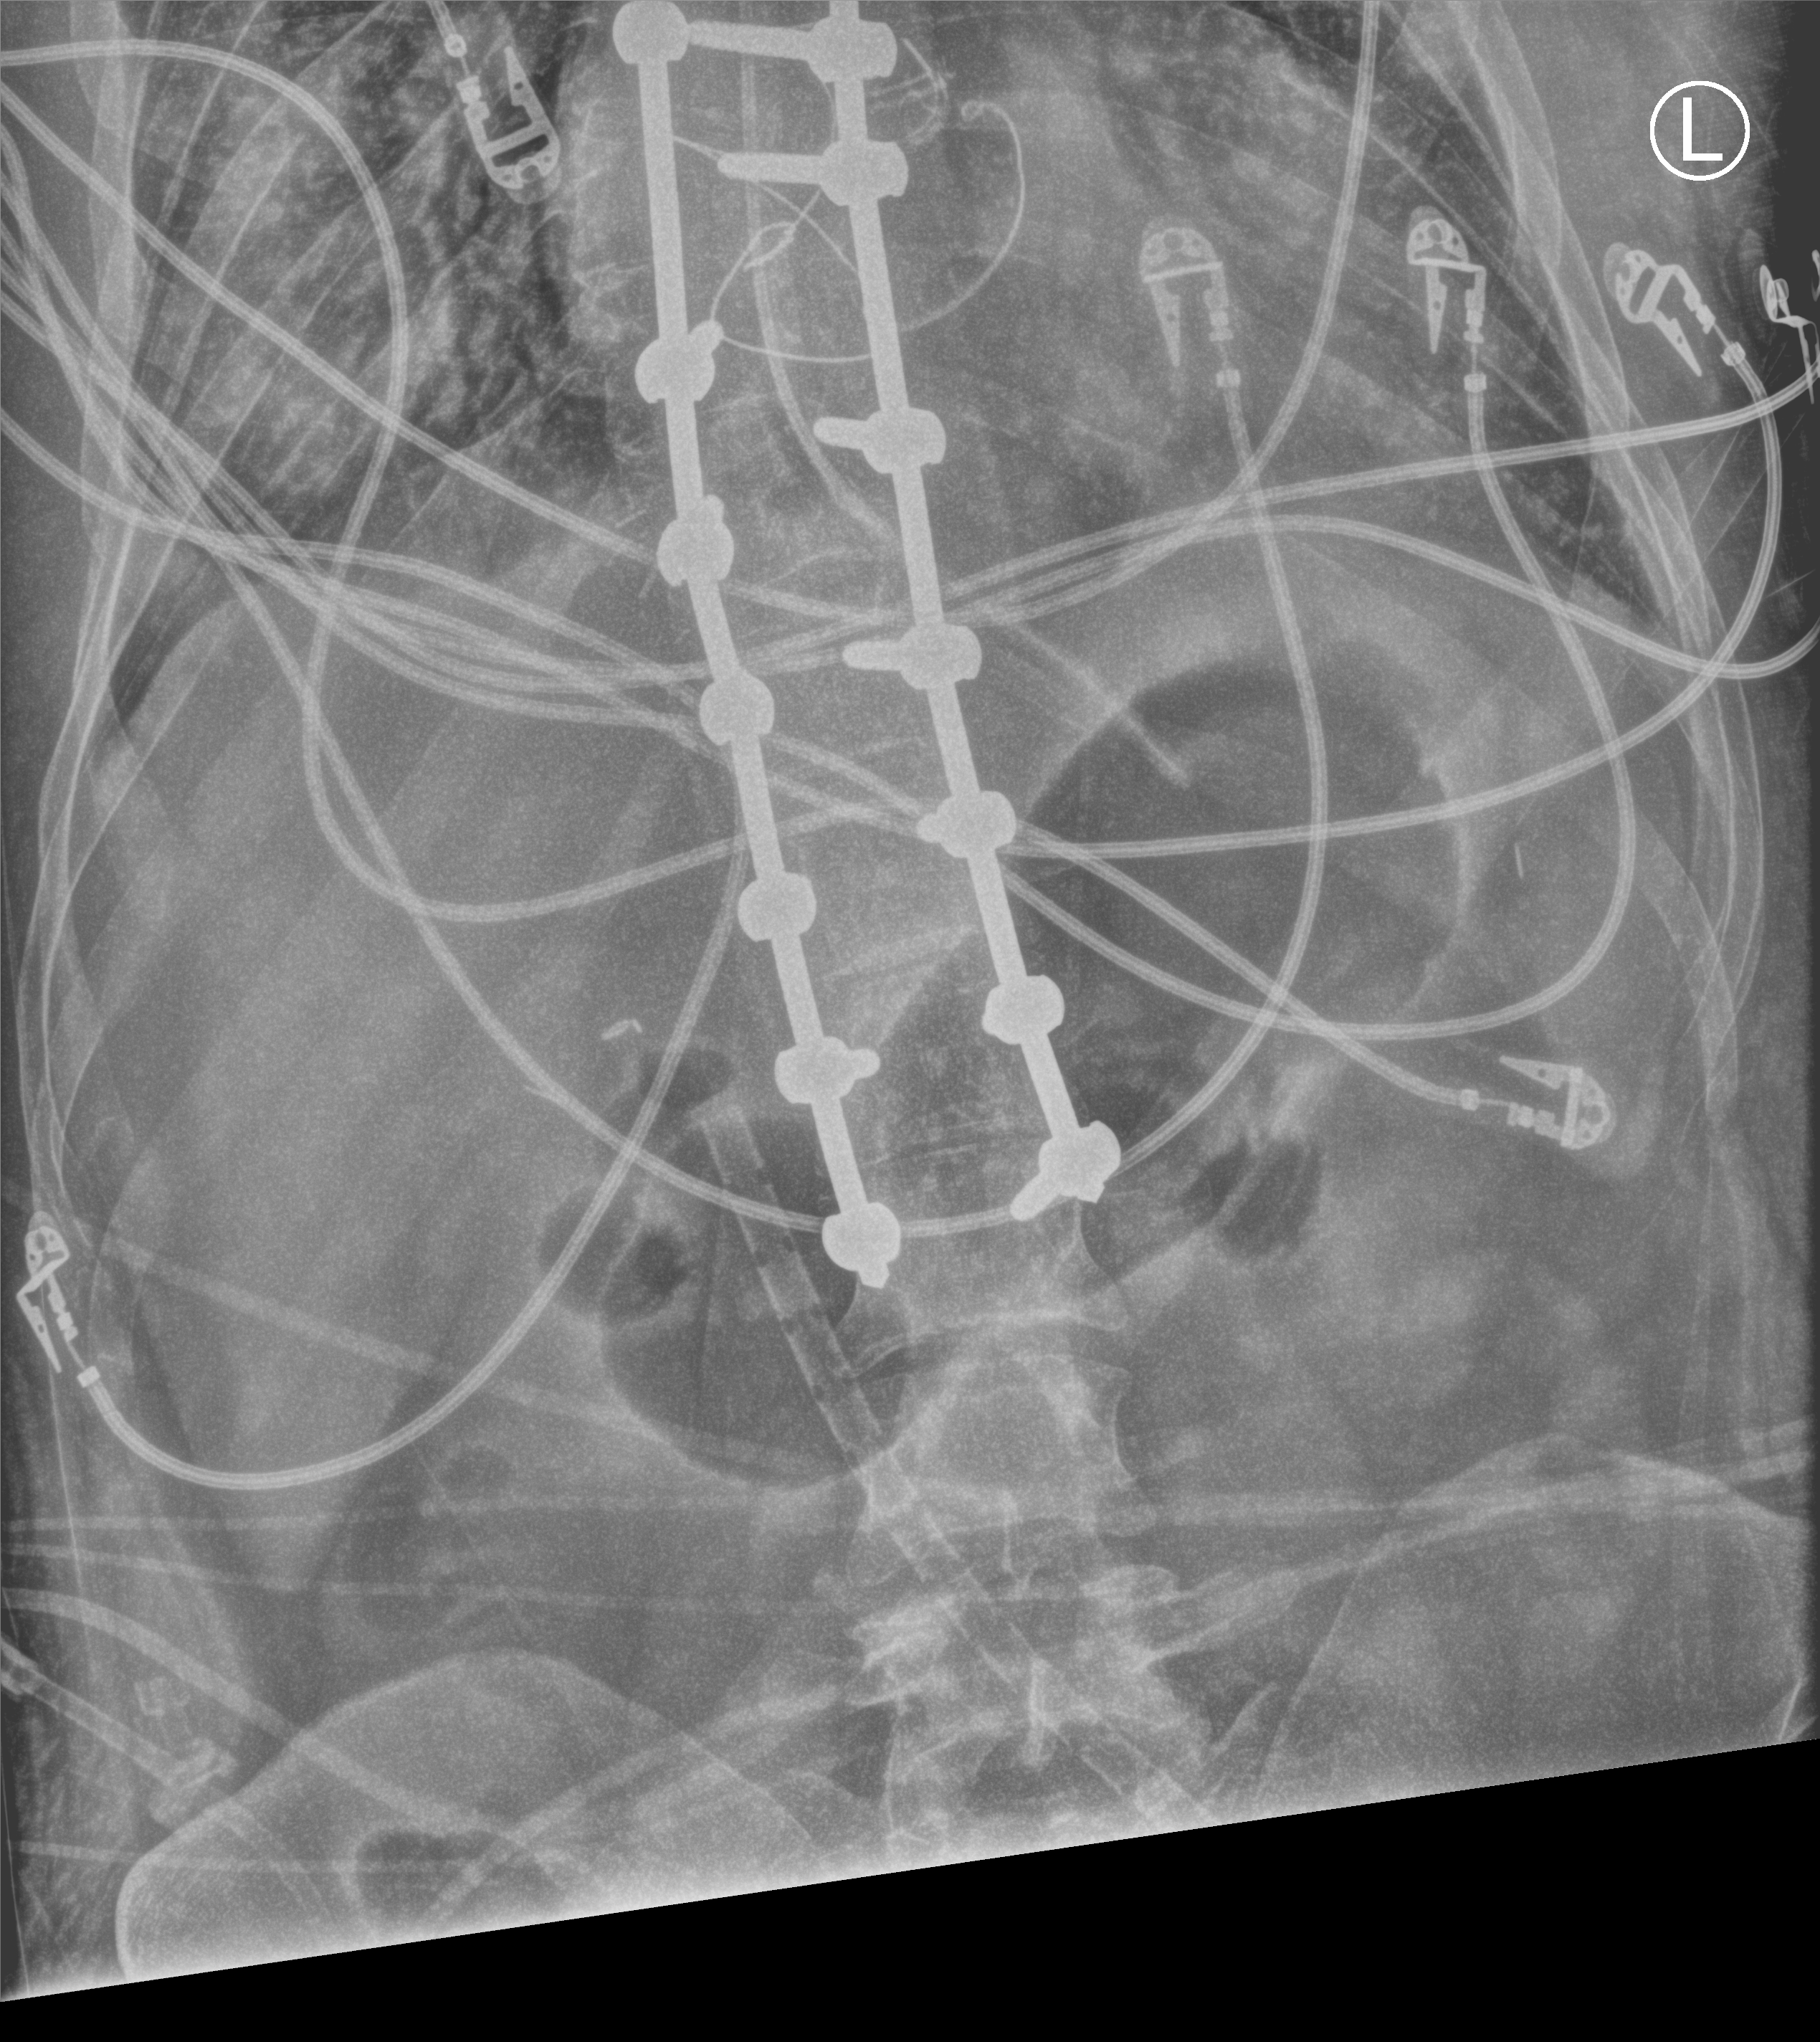
Abdomen radiograph (computed radiography); anteroposterior (AP) projection. Patient hospitalised with COVID-19, aged 18–59 years.
From the hospital-stay record, not from the radiograph (when in the stay this image was taken is not recorded): mechanically ventilated during this hospital stay: yes.